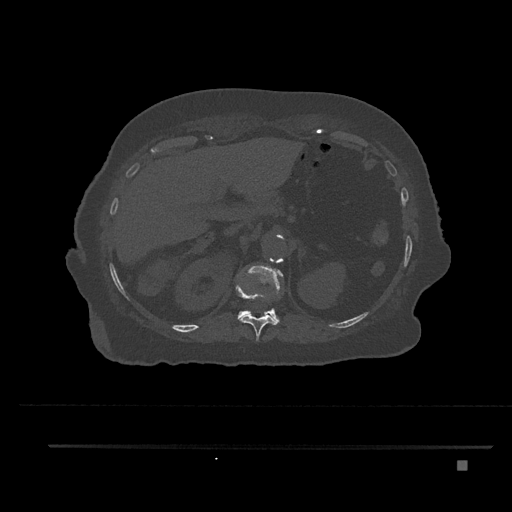
CT including the spine, one axial slice. Position 294 of 797 along the scan axis. Reconstruction kernel Br40s/3. Bone window (W 1800 / L 400 HU). 512 × 512 image matrix, field of view 437 × 437 mm. Patient: female, 76 years. Case-level facts recorded for this patient, not image findings: primary cancer: lung; vertebrae with lytic lesions (as recorded): T11, L3.
Structures marked on this image (semi-automatic segmentation, software-assisted and operator-edited):
- T11 vertebra: bounding box (x1, y1, x2, y2) in pixels: (236, 286, 278, 341)
- T12 vertebra: (237, 266, 282, 323)